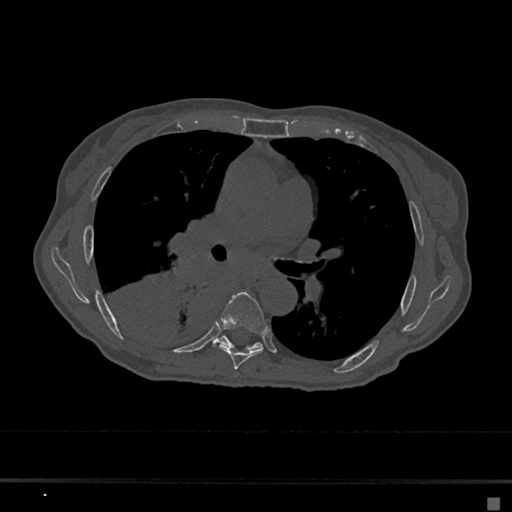
CT including the spine, one axial slice; slice 402 of 797 in the series (ordered by position); 120 kVp; bone window (W 1800 / L 400 HU); 512 × 512 image matrix, field of view 360 × 360 mm. Female patient, age 68 years. Case-level facts recorded for this patient, not image findings: primary cancer: renal.
Structures marked on this image (semi-automatic segmentation, software-assisted and operator-edited):
- T6 vertebra: bounding box [x1, y1, x2, y2] px = [213, 291, 268, 370]
- T7 vertebra: [216, 336, 262, 350]